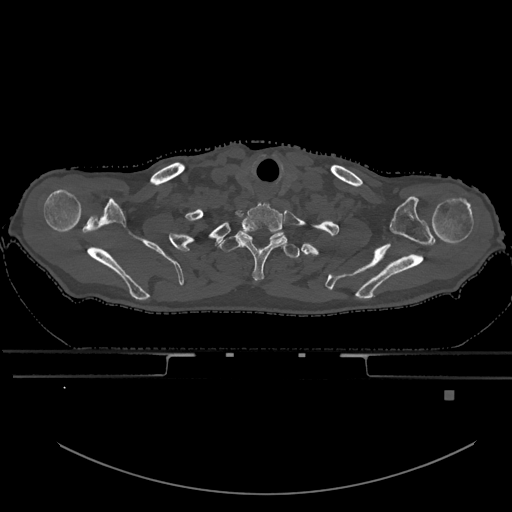
CT including the spine, one axial slice. Slice 559 of 969 in the series (ordered by position). Bone window (W 1800 / L 400 HU). 512 × 512 image matrix, field of view 456 × 456 mm. Patient: male, 82 years. From the clinical record (not read from this slice): primary cancer: prostate.
Outlined on this slice (semi-automatic segmentation, software-assisted and operator-edited):
- T1 vertebra: bounding box (x1, y1, x2, y2) in pixels: (219, 234, 300, 259)